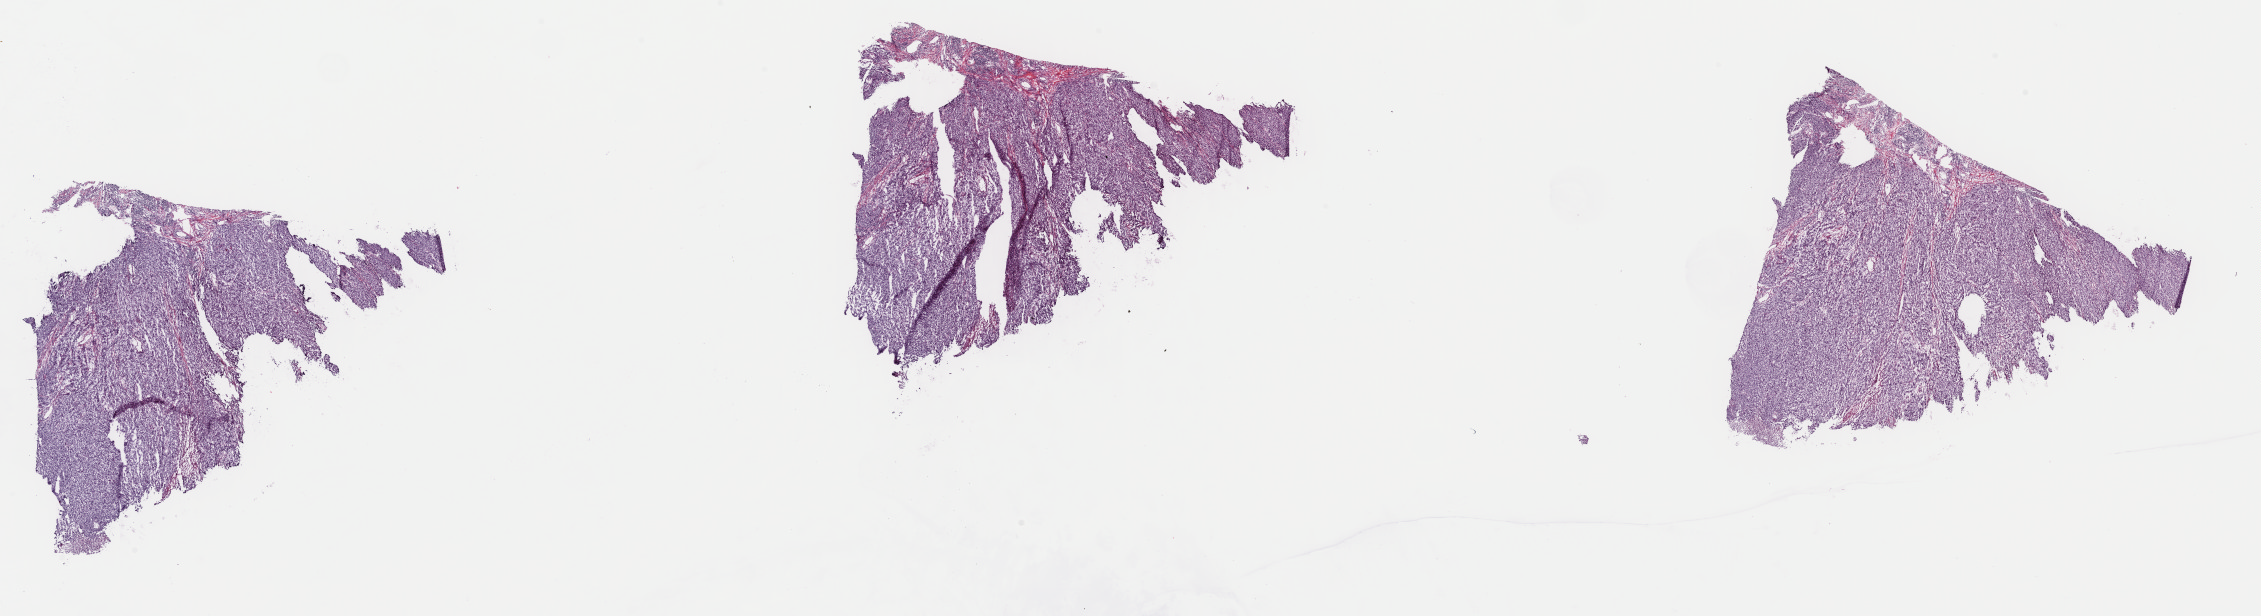
Whole-slide histology image, Hematoxylin and eosin (H&E) stained — low-resolution overview of the scanned area, about 35.7 x 9.7 mm (acquisition: 40x scan); frozen section; sample: primary tumour, skin. Patient: female, age at initial diagnosis 58 years. Pathologist review of this section (percent, as recorded): tumour cells 75%, tumour nuclei 80%, normal cells 0%, stromal cells 20%, necrosis 5%. Infiltration values recorded for this section: lymphocyte infiltration 5%, monocyte infiltration 0%, neutrophil infiltration 0%.
• TNM: T4b N0 M0
• diagnosis: Malignant melanoma, NOS
• AJCC pathologic stage: IIC (7th edition)